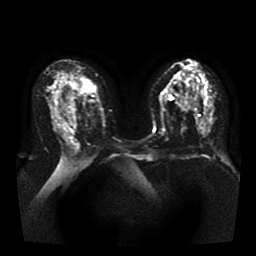
Breast MRI, one axial slice. Slice 21 of 41 in the series (ordered by position). Diffusion-weighted series; image 2 of 4 stored at this slice position (different b-values; order by instance number). 1.5 T. 256 × 256 image matrix. Female patient.
Annotated regions visible in this slice (outlined manually by an expert reader):
- tumour on diffusion-weighted imaging: bounding box (x1, y1, x2, y2) in pixels: (80, 90, 90, 100)